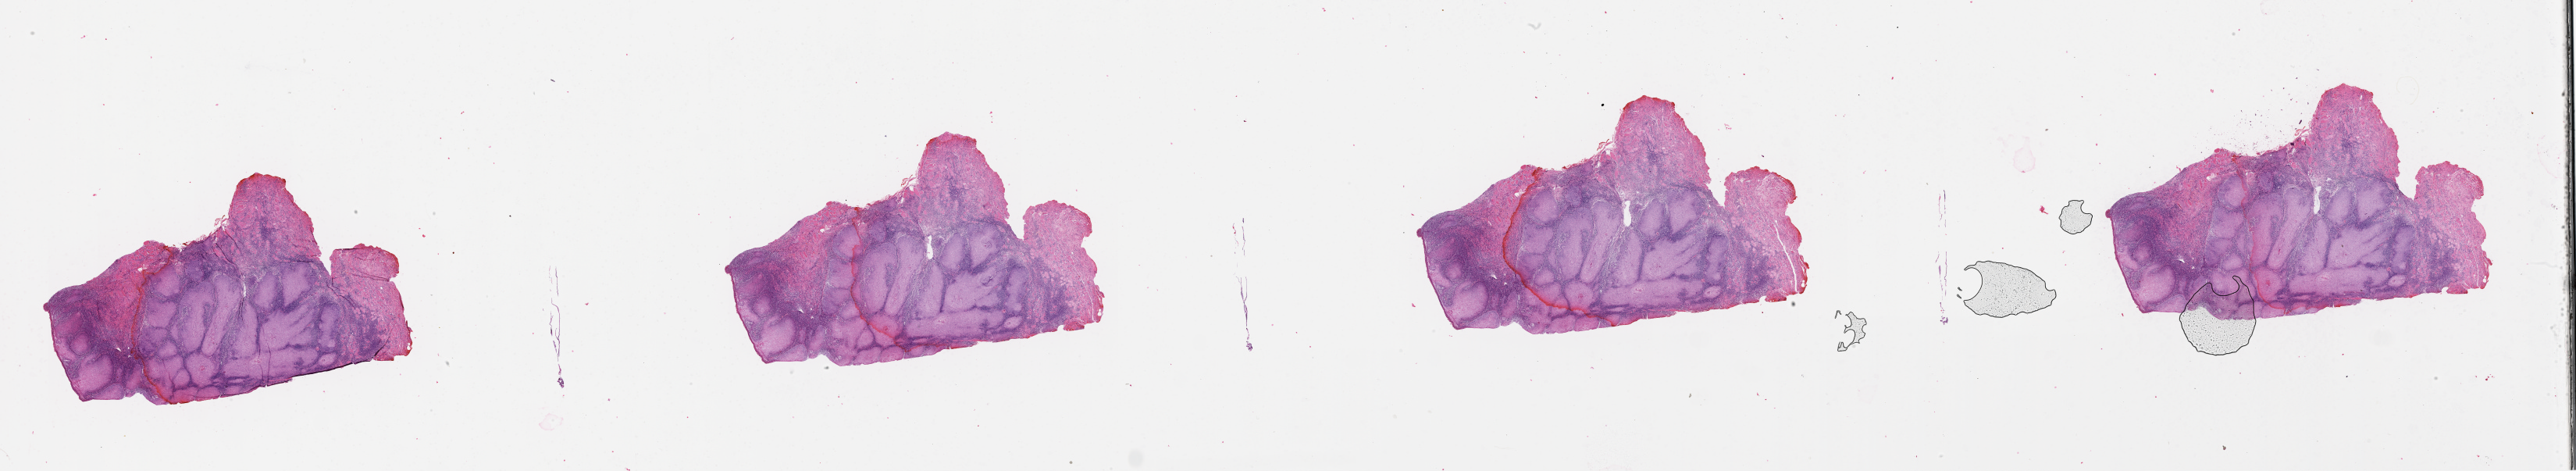
H&E-stained whole-slide image, whole scanned area (about 53.1 x 9.7 mm) shown as a low-resolution overview. Tumour tissue sample, sampled site: buccal mucosa. 69-year-old male patient. Histologic grade: G2 (moderately differentiated). Slide review estimates, as recorded: tumour nuclei 80%, necrosis 5%.
• primary tumour site (as recorded): oral cavity
• diagnosis: Squamous cell carcinoma, NOS (cheek mucosa)
• AJCC pathologic stage: I